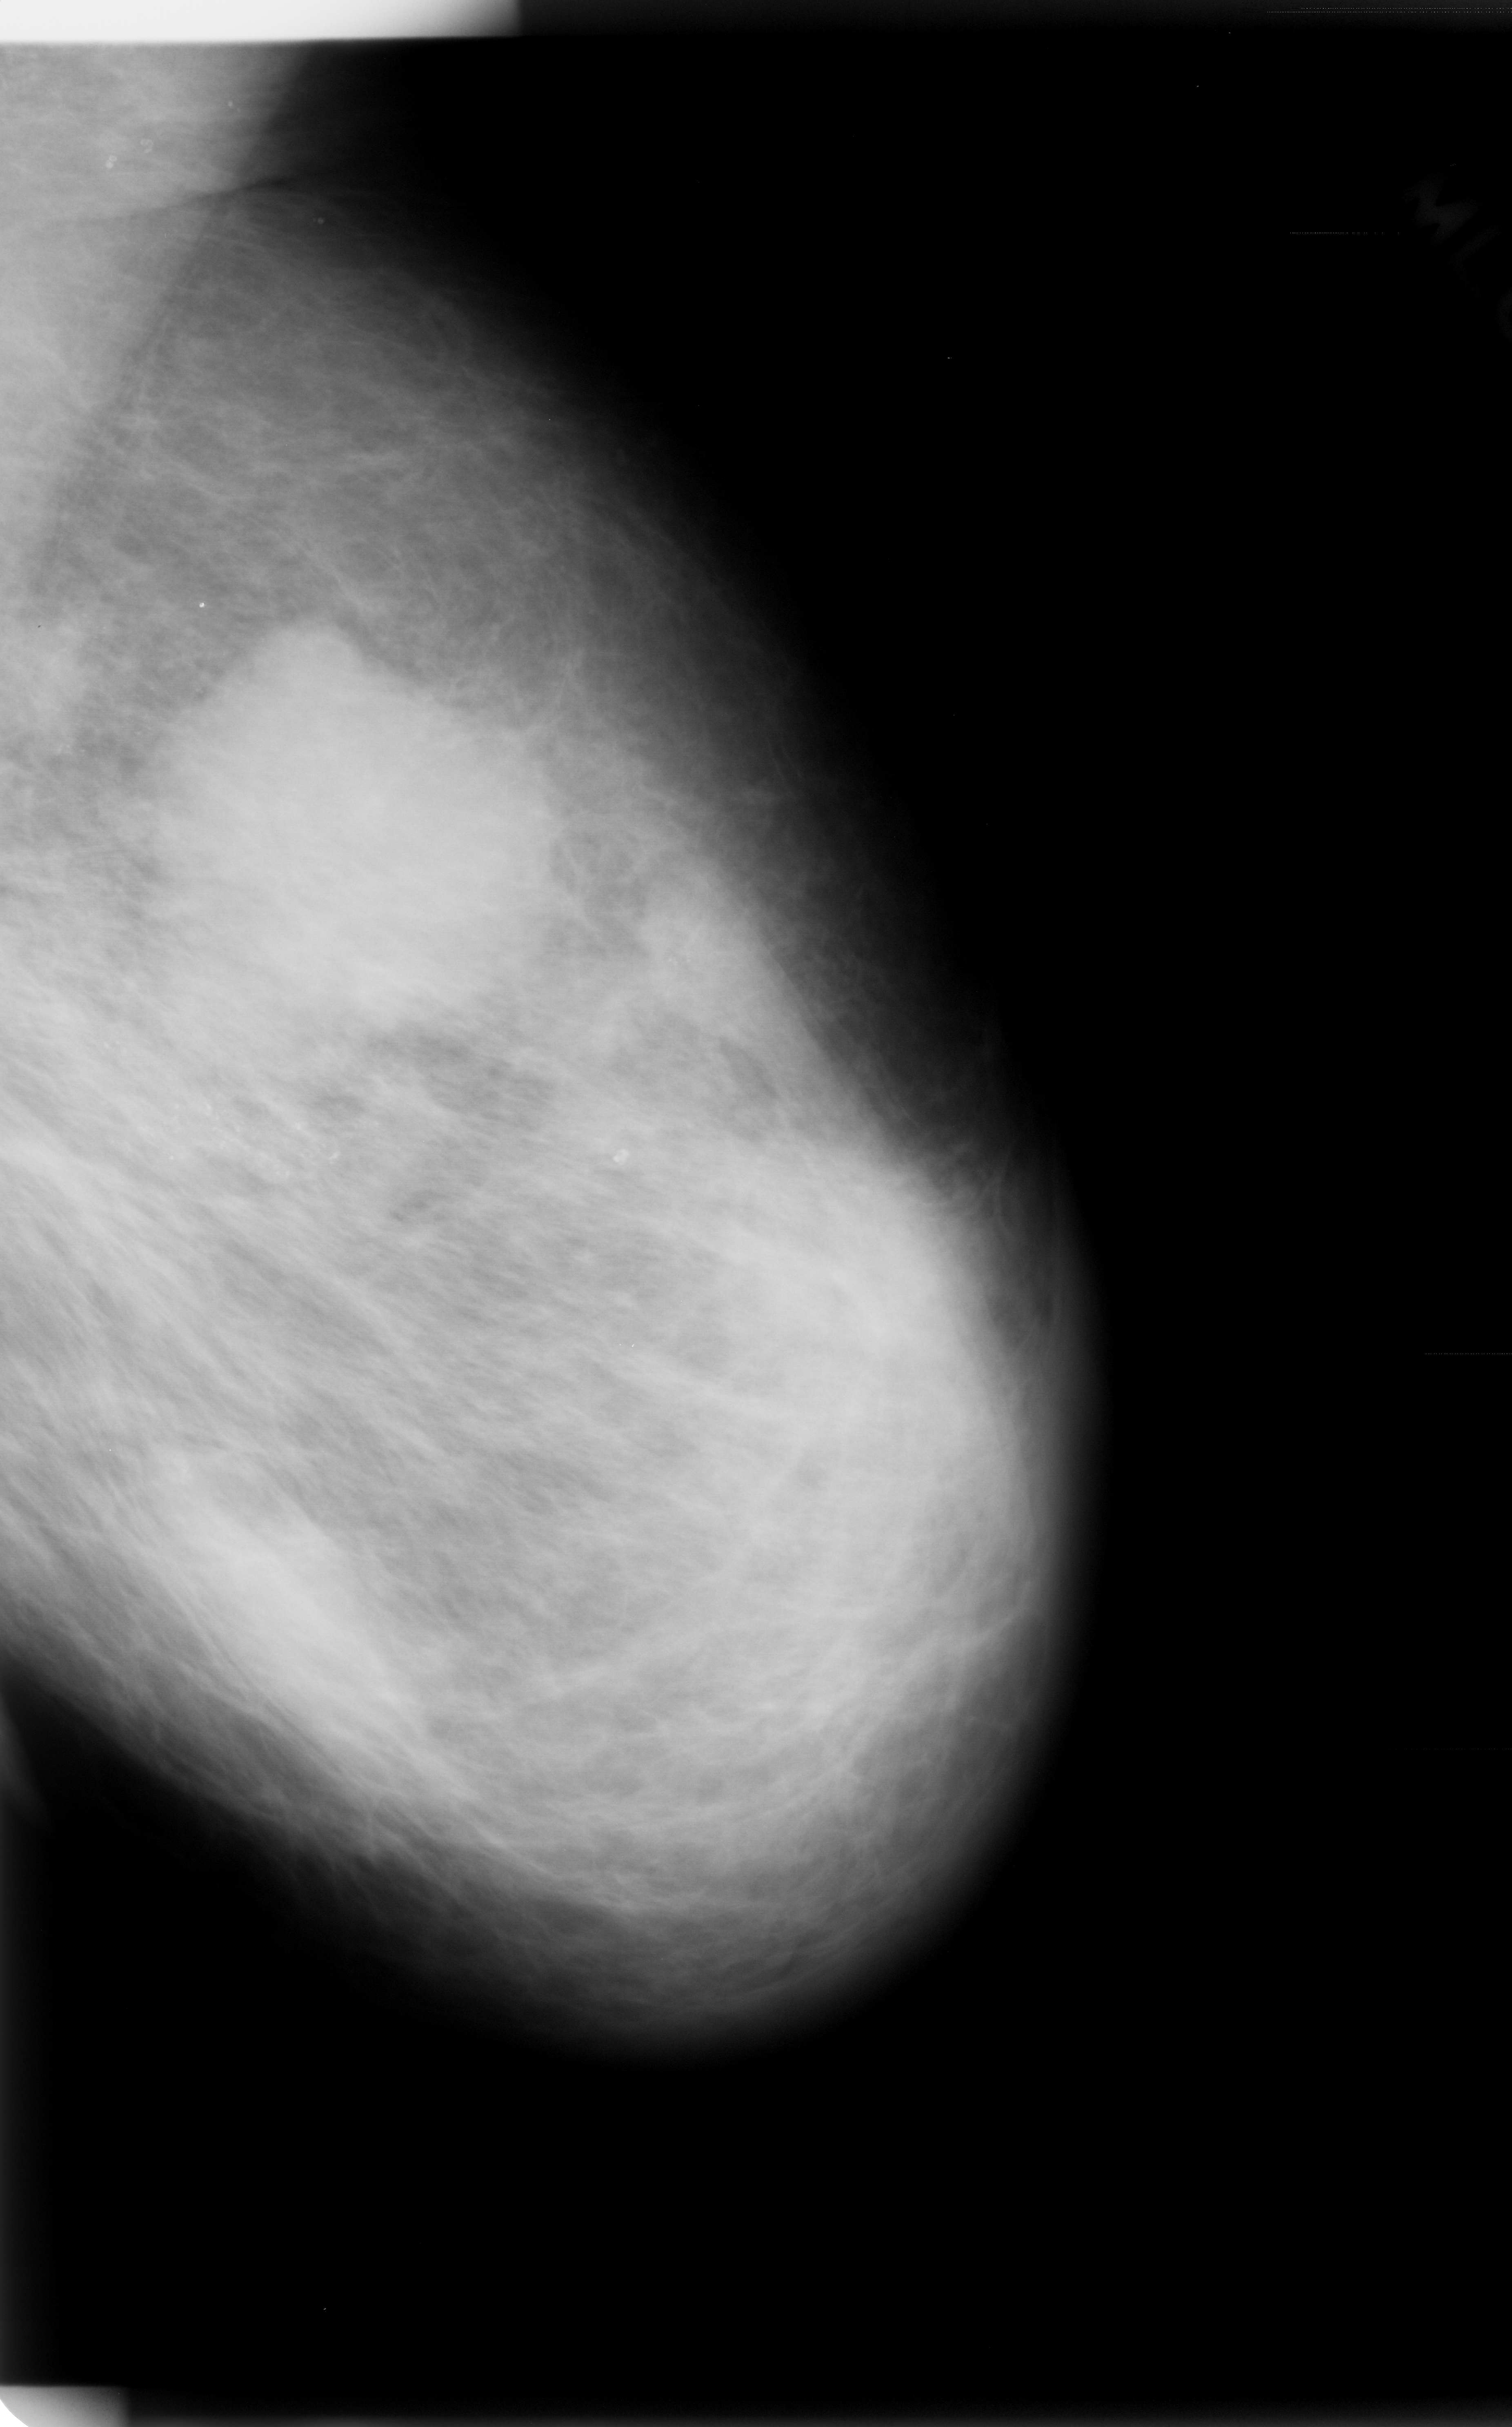
Scanned film-screen mammogram, left breast, mediolateral oblique (MLO) view, BI-RADS breast density category 2 (scale 1–4).
Calcifications, morphology pleomorphic, distribution segmental; BI-RADS assessment category 5; subtlety rating 5 on a 1 (subtle) to 5 (obvious) scale; pathology (as recorded): malignant.